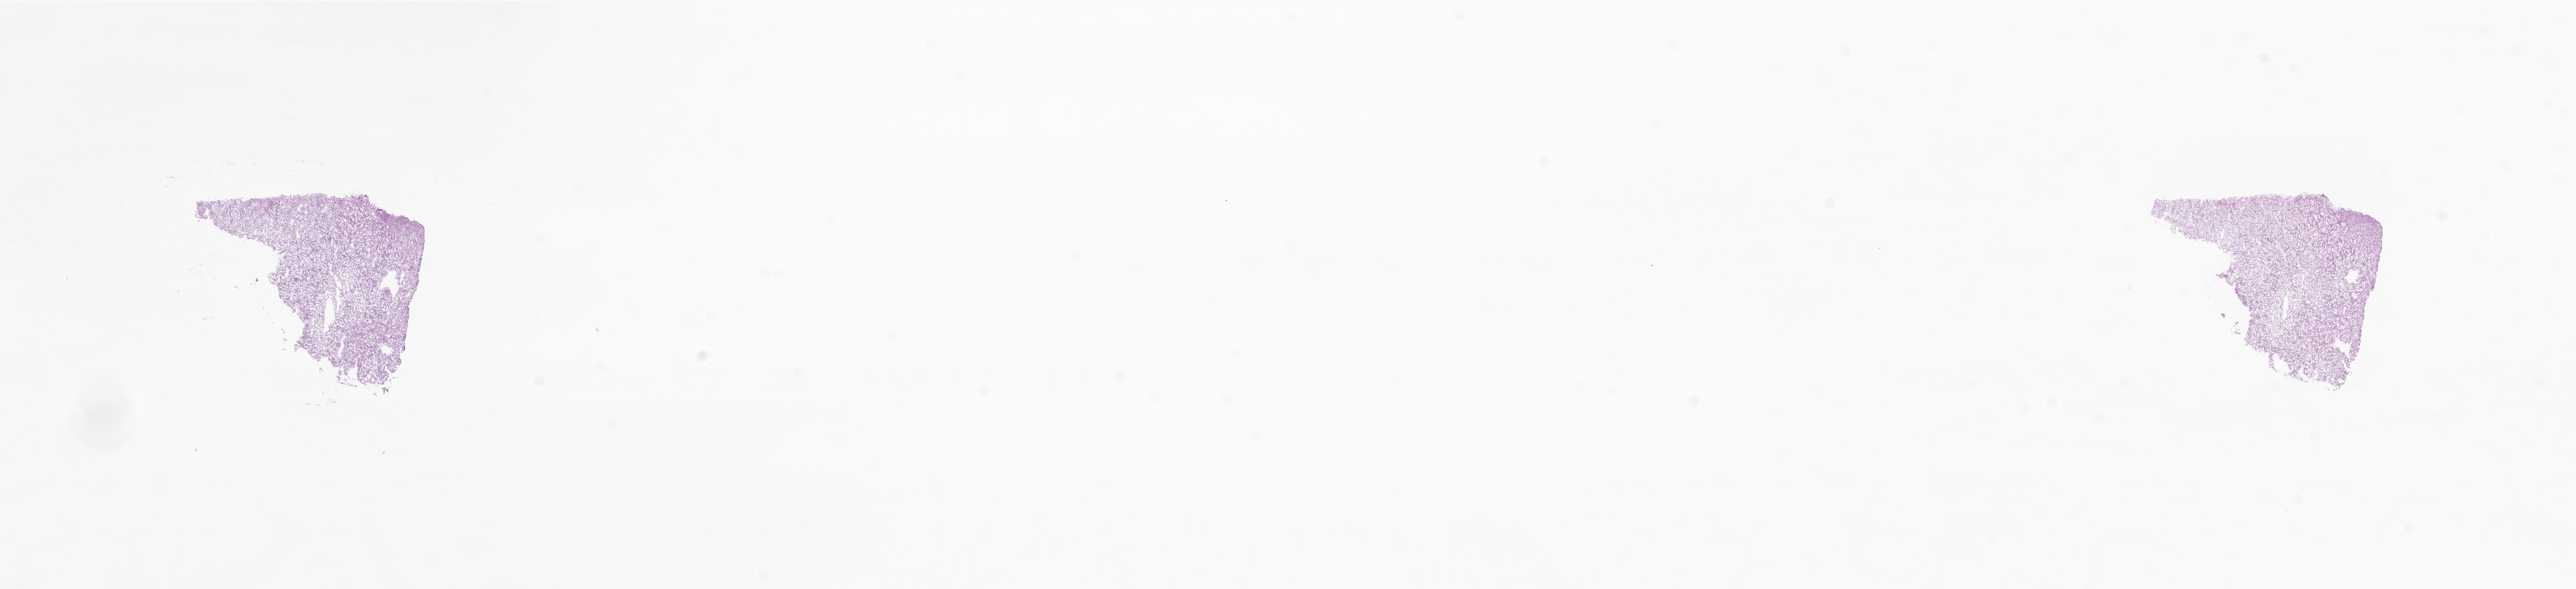
Digitized haematoxylin and eosin-stained section of tumor tissue from the frontal lobe, whole scanned area (about 24.4 x 5.6 mm) shown as a low-resolution overview. Cryosection (OCT / tissue freezing medium). Patient female; age 203 months.
Diagnosis (ICD-O-3 morphology term): Dysembryoplastic neuroepithelial tumor.